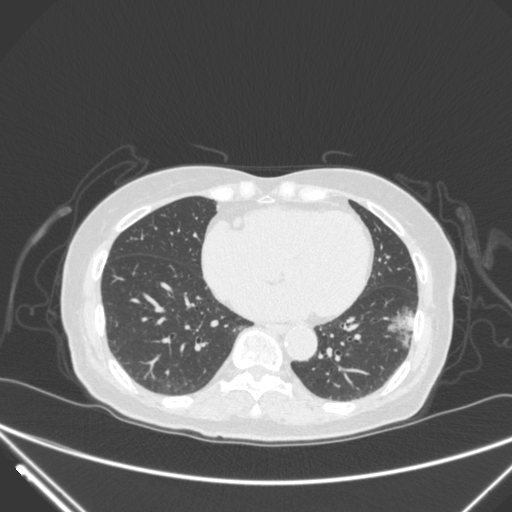
Chest CT, one axial slice. Position 113 of 310 along the scan axis. Lung window (W 1500 / L -600 HU). 512 × 512 image matrix, field of view 377 × 377 mm. Female patient, age 82 years. Case-level facts recorded for this patient, not image findings: clinical TNM (as recorded): T1c N0 M0; histopathological grade: G2.
Structures marked on this image (rectangle marked by the reading radiologist):
- lung tumour (recorded histology: adenocarcinoma): bounding box [x1, y1, x2, y2] px = [384, 298, 415, 344]